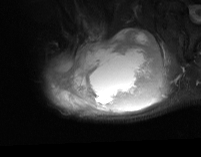
MRI of an extremity soft-tissue mass, one axial slice; position 49 of 74 along the scan axis; STIR; MR volume resampled by the dataset authors to the PET/CT grid (not the native acquisition matrix); 3.27 mm slice thickness; 201 × 157 image matrix, field of view 196 × 153 mm. Male patient. Case-level facts recorded for this patient, not image findings: histological type: pleiomorphic spindle cell undifferentiated; grade: high; site of the primary tumour: right parascapusular.
Outlined on this slice (expert contour drawn on MRI and transferred to this co-registered scan by the dataset authors):
- gross tumour volume including surrounding oedema: box from (x=44, y=20) to (x=182, y=117) px
- gross tumour volume (mass): (x=49, y=27)–(x=164, y=113)